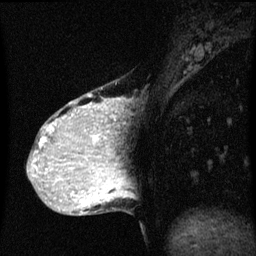
Breast MRI (dynamic contrast-enhanced), one sagittal slice; slice 18 of 60 in the series (ordered by position); dynamic contrast-enhanced series, image 2 of 3 at this slice position (ordered by acquisition); 1.5 T; TE 4.2 ms, TR 8 ms; 2 mm slice thickness; 256 × 256 image matrix. Patient: female, 36 years.
Structures marked on this image (semi-automatically segmented with operator editing):
- analysis volume of interest (the breast-tissue region the enhancement analysis was run in; not a lesion): bounding box <33,84,121,169> (left, top, right, bottom; pixels)
- tumour enhancement mask (voxels above the 70 % enhancement threshold inside the analysis volume of interest): <35,98,120,169>